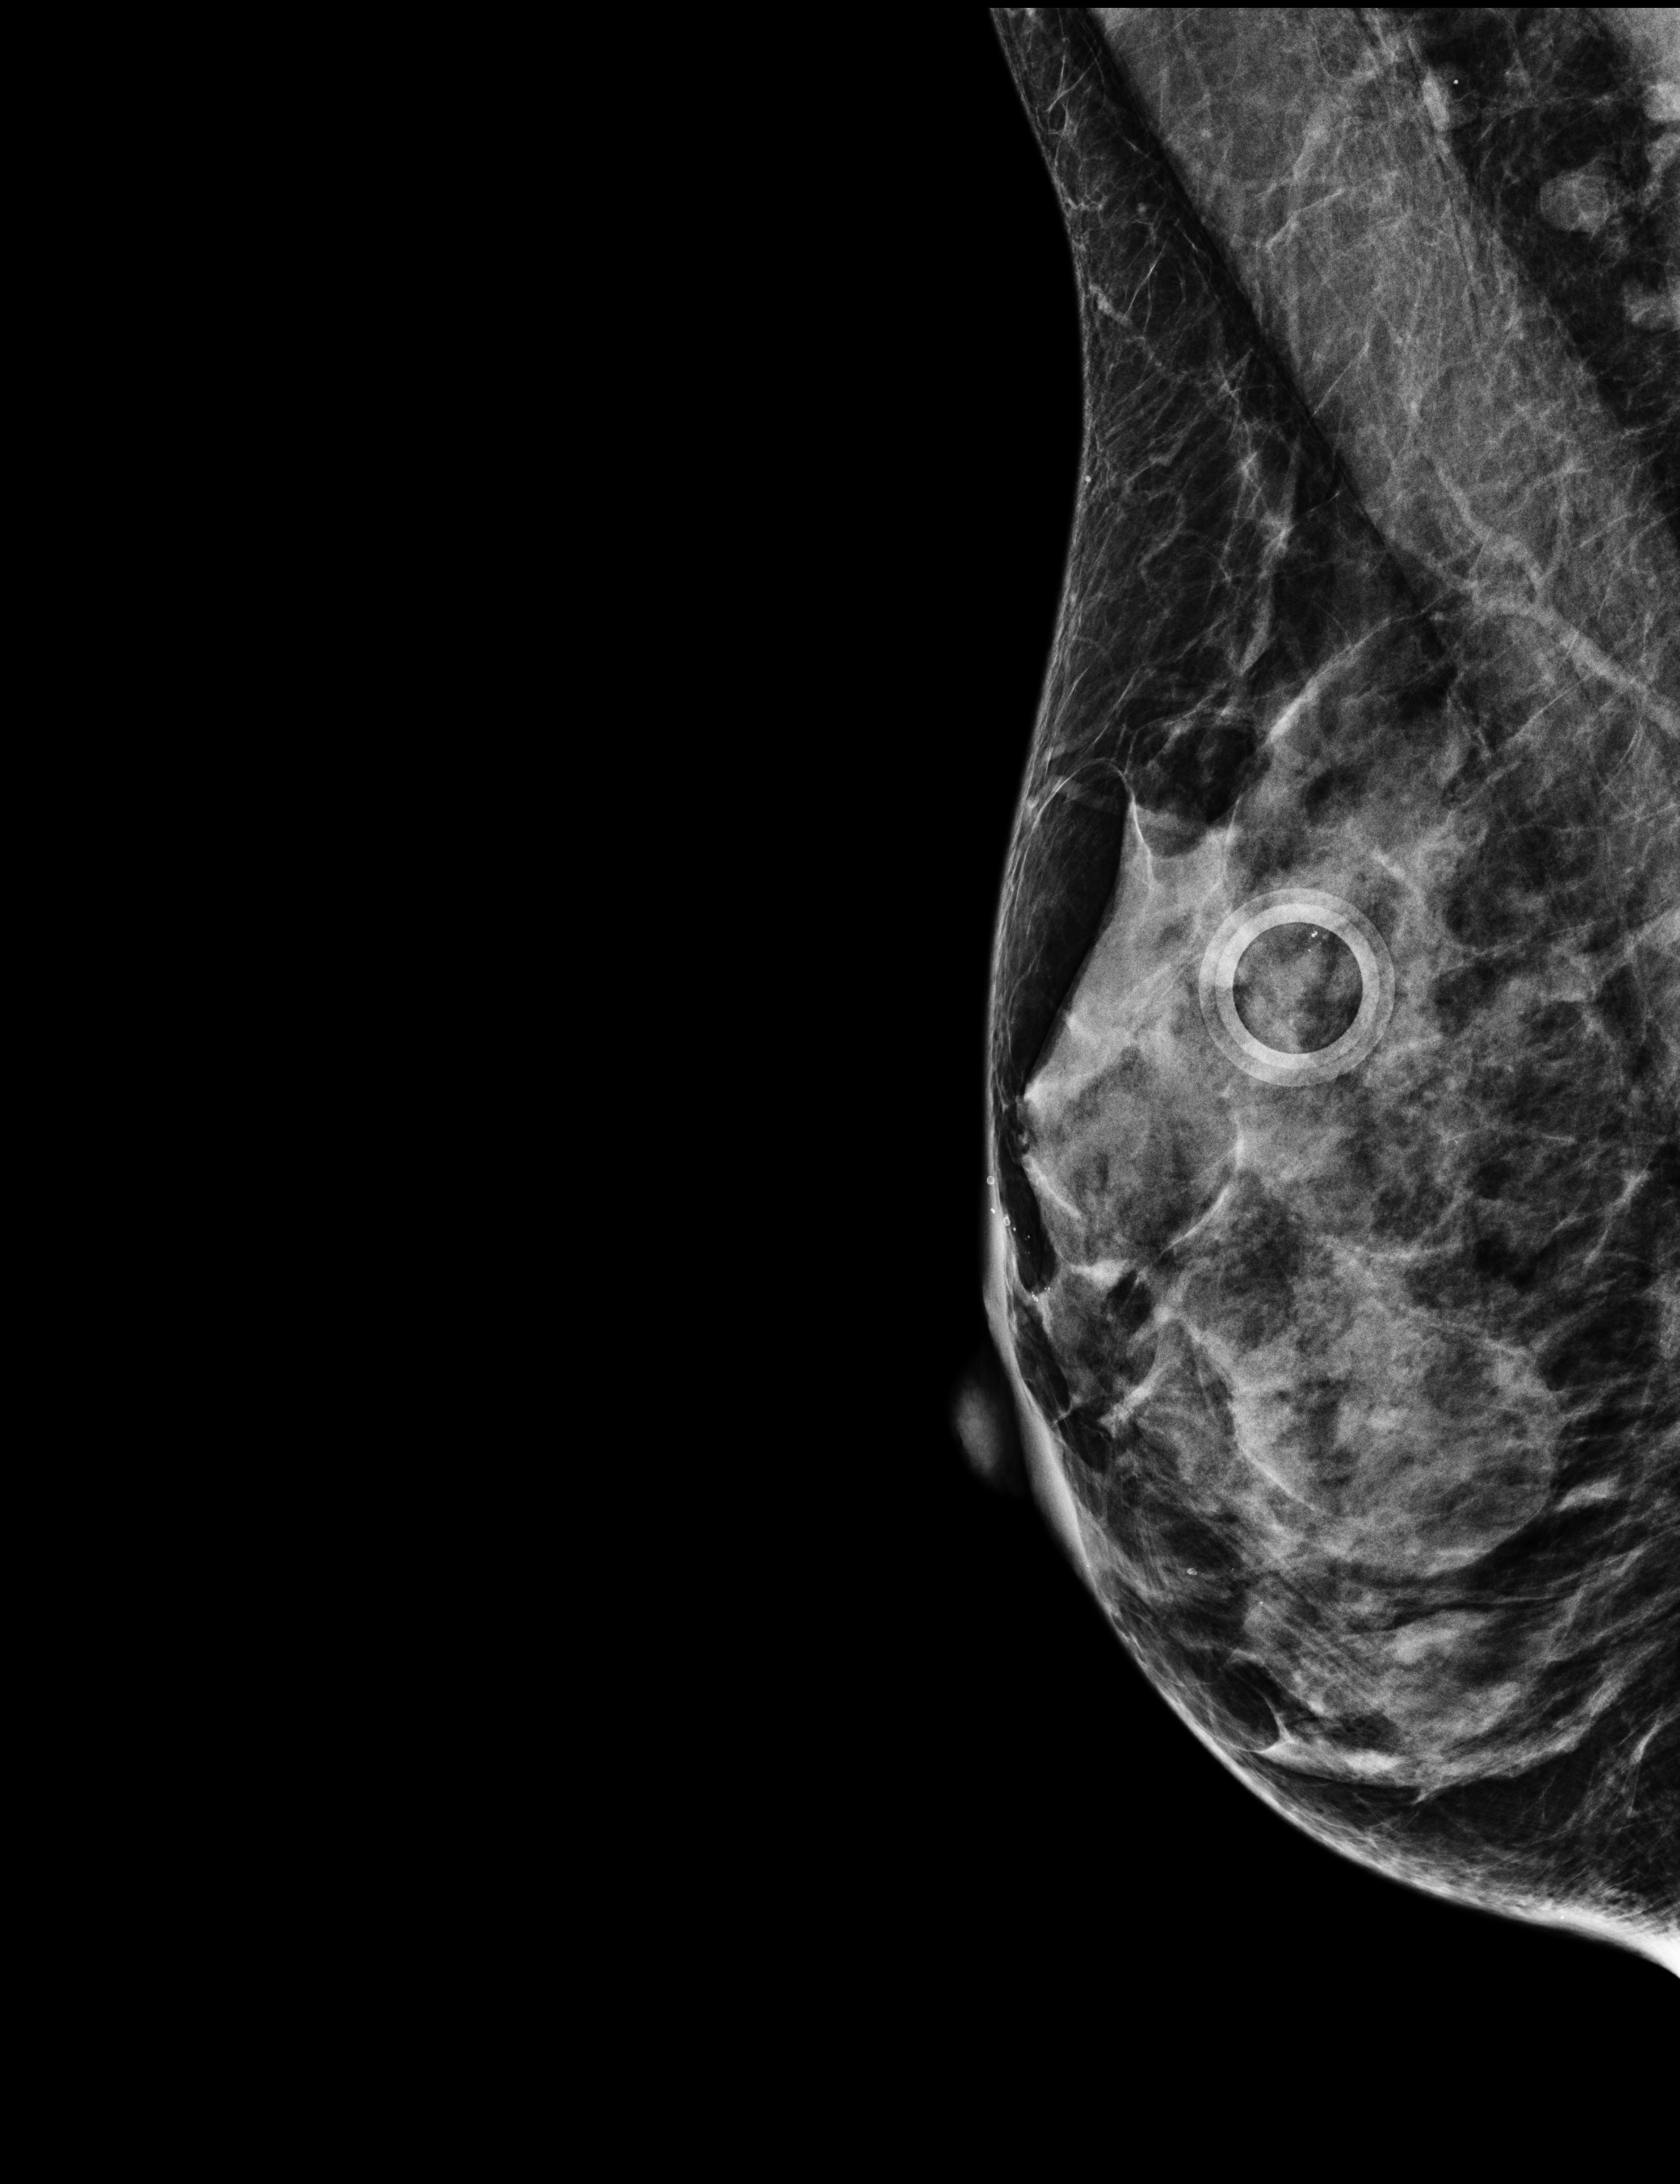
Annual screening mammography examination; compressed breast thickness 42 mm. Female patient, age 57 years.
Image type: full-field digital mammogram. Breast: right. Projection: mediolateral oblique (MLO) view.